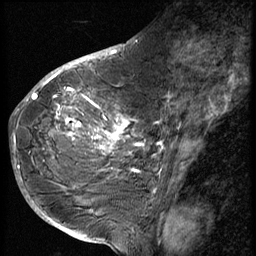
Breast MRI (dynamic contrast-enhanced), one sagittal slice. Slice 27 of 56 in the series (ordered by position). 3 images stored at this slice position (order not interpretable as contrast timing). 1.5 T. TE 4.2 ms, TR 9 ms. 2.5 mm slice thickness. 256 × 256 image matrix, field of view 180 × 180 mm. Female patient, age 49 years. Case-level facts recorded for this patient, not image findings: setting: breast cancer imaged before/during neoadjuvant chemotherapy; receptor status: HER2-positive.
Structures marked on this image (semi-automatic segmentation, software-assisted and operator-edited):
- analysis volume of interest (the breast-tissue region the enhancement analysis was run in; not a lesion): box from (x=37, y=85) to (x=134, y=207) px
- tumour enhancement mask (voxels above the 140 % enhancement threshold inside the analysis volume of interest): (x=38, y=85)–(x=134, y=171)